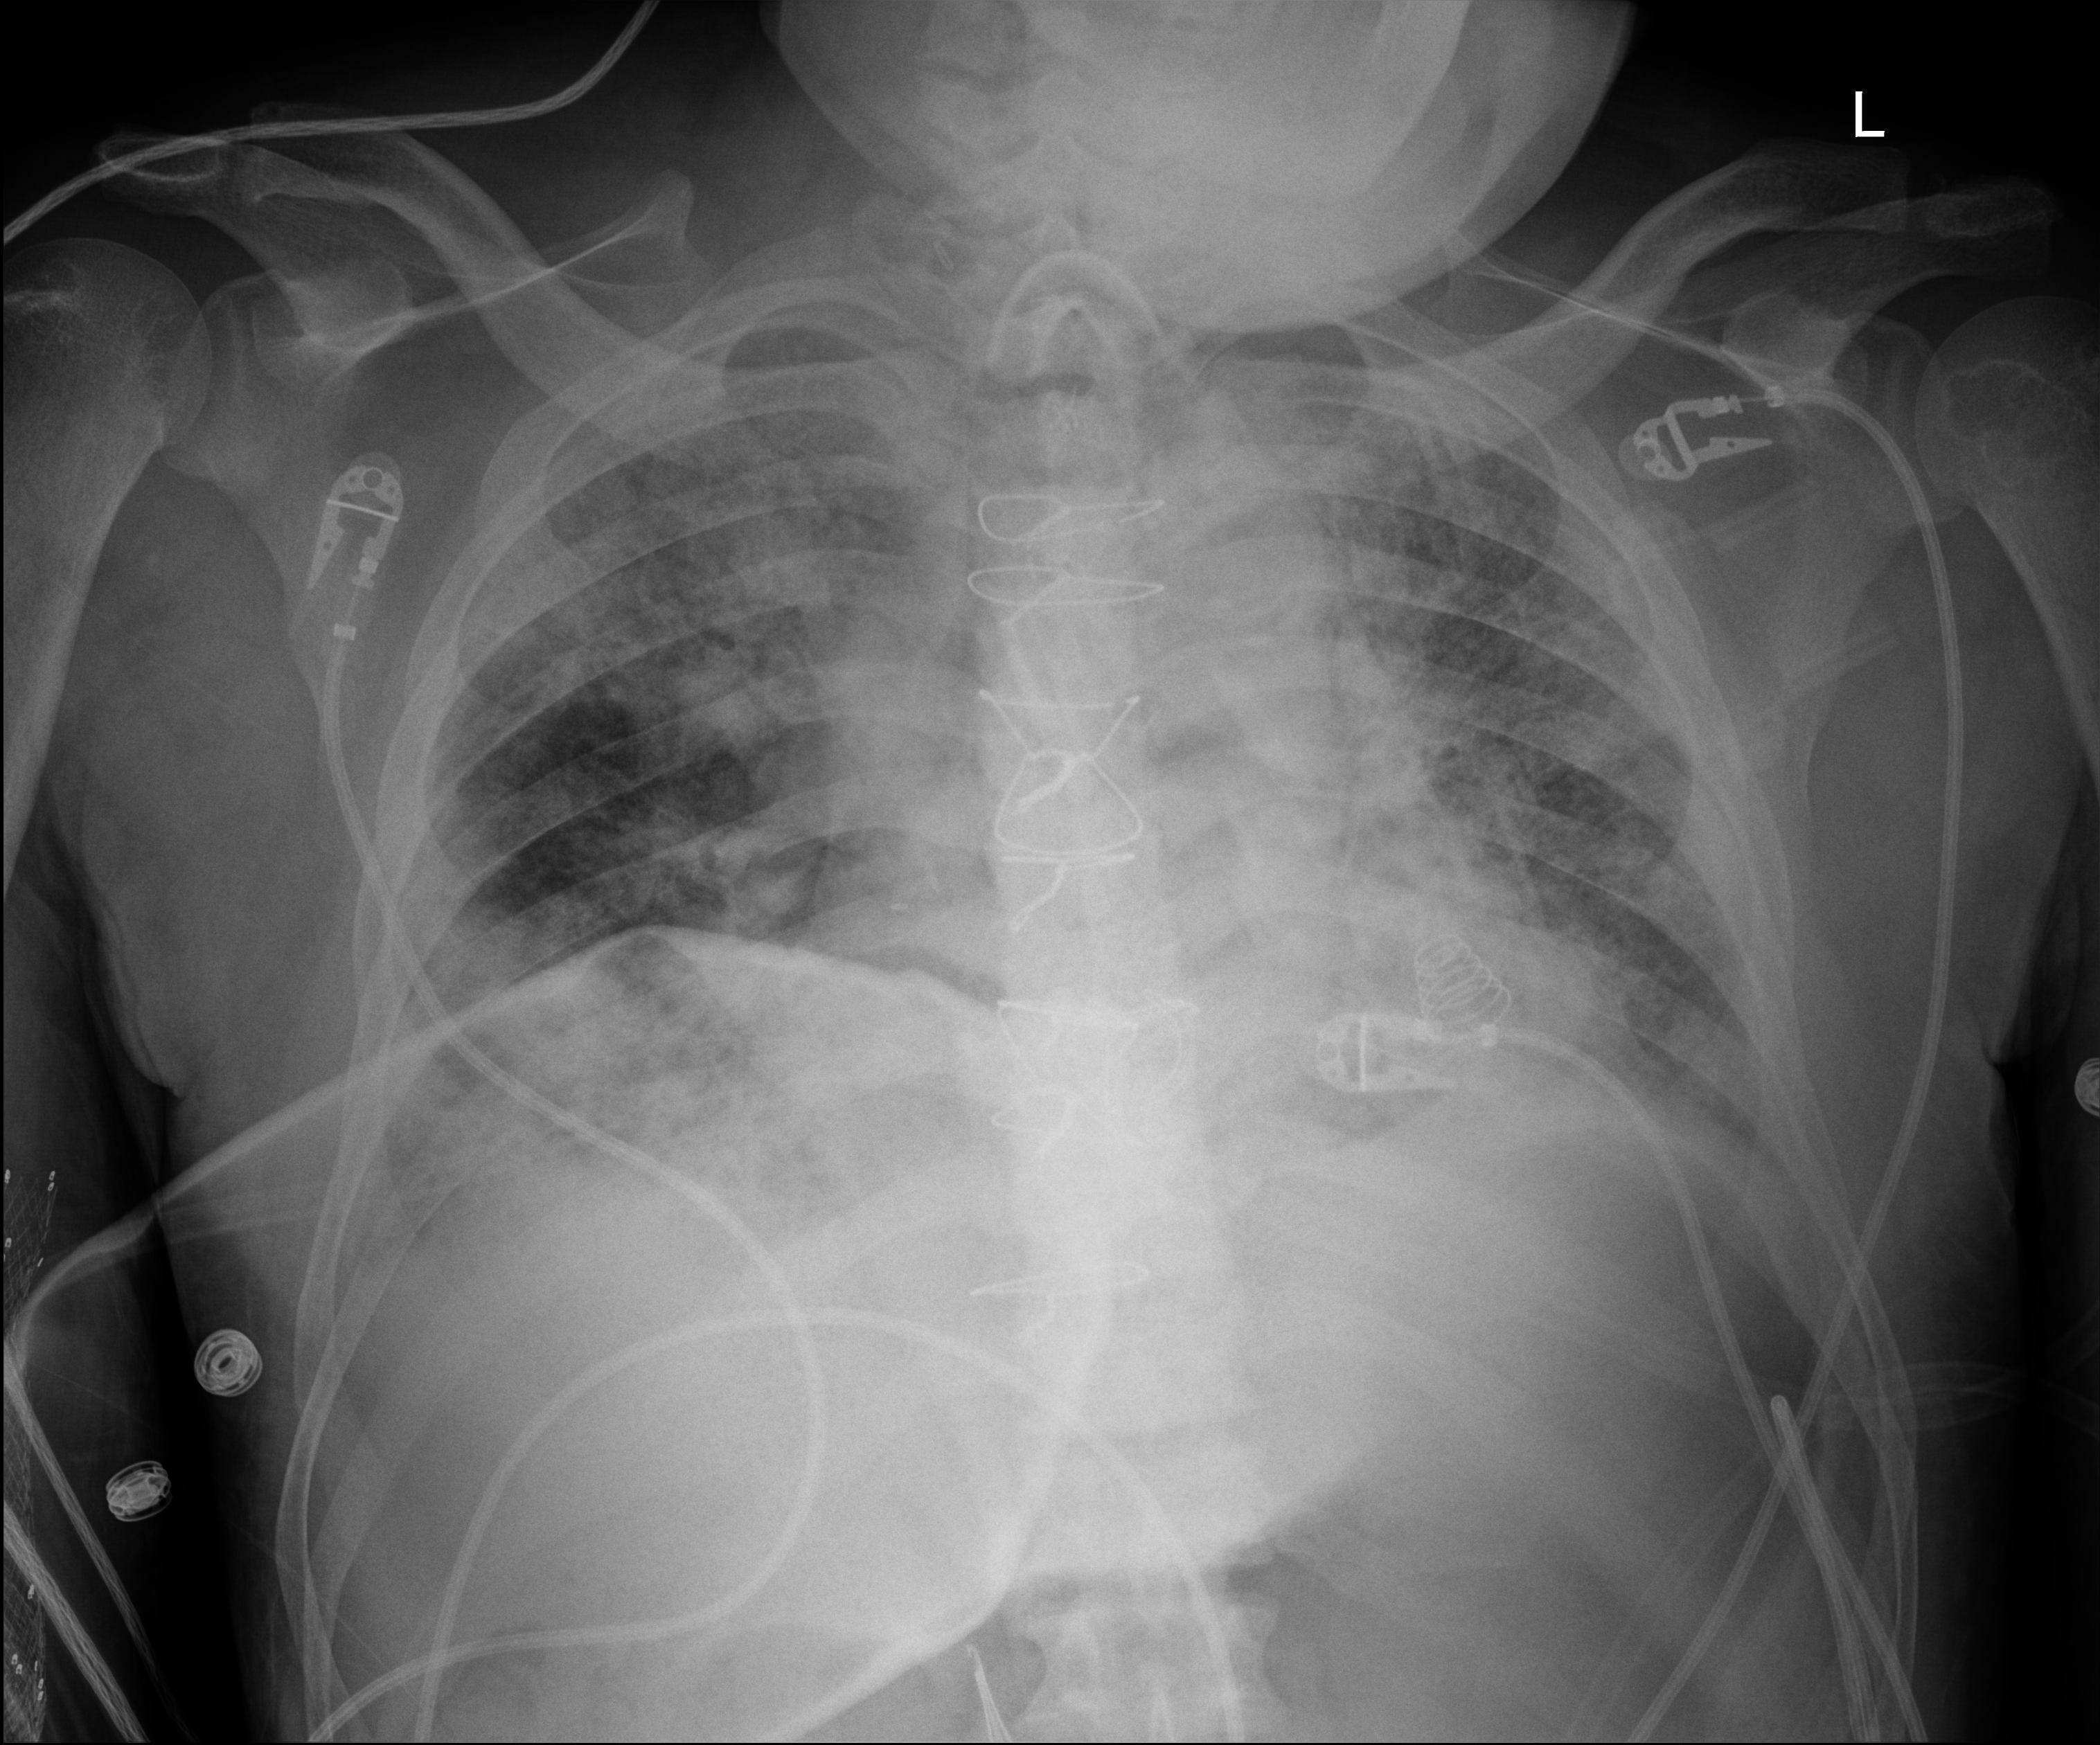
Portable chest radiograph, anteroposterior (AP) projection. Male patient hospitalised with COVID-19, age 60–74 years.
Hospital-stay facts (about this admission, not read from this image; timing relative to this image not recorded): admitted to intensive care during this hospital stay: yes; other chronic lung disease (admission record): no.